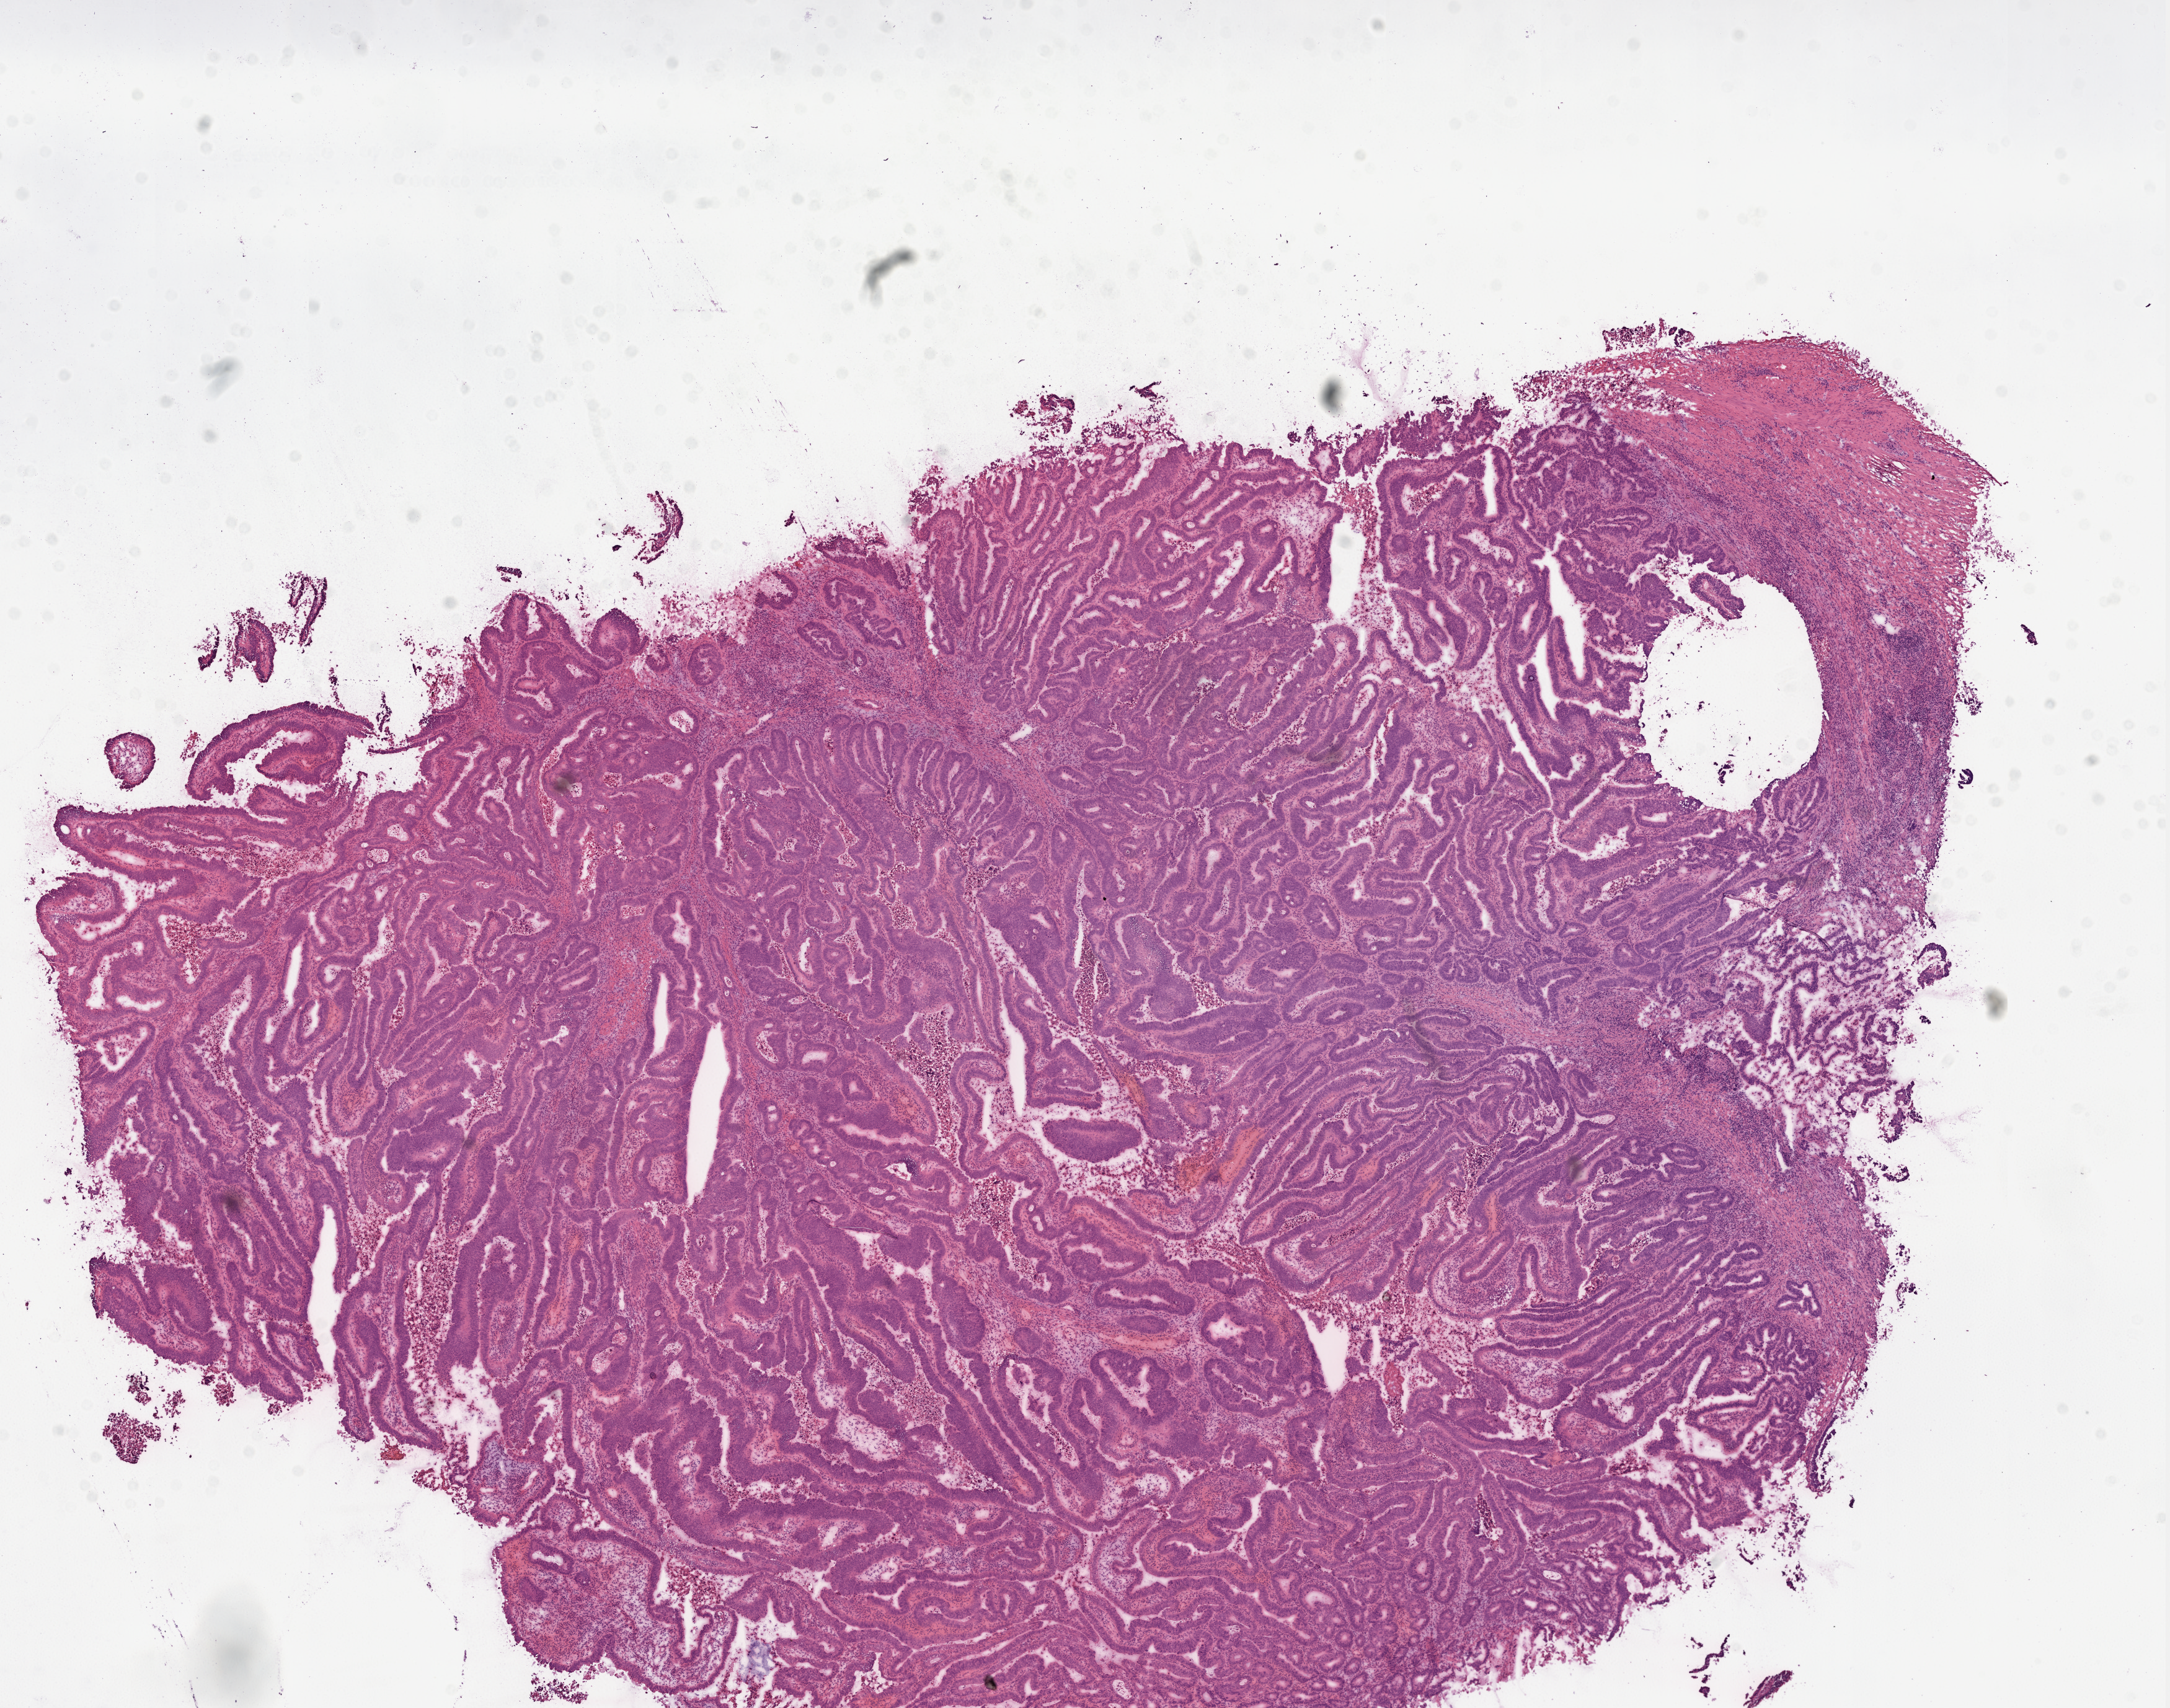
Hematoxylin and eosin (H&E) stained whole-slide image — whole scanned area (about 14.0 x 11.1 mm, slide scanned at 20x) shown as a low-resolution overview, frozen section from the top of the tissue portion, colon, primary tumour sample. Female patient; age at initial diagnosis 54 years.
Histologic diagnosis: Adenocarcinoma, NOS.